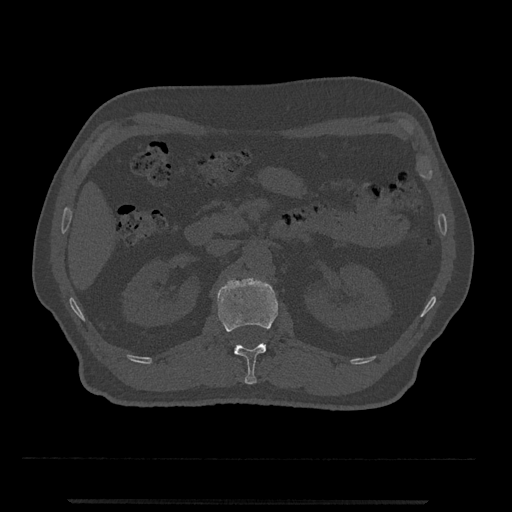
CT including the spine, one axial slice. Position 321 of 797 along the scan axis. 120 kVp. Bone window (W 1800 / L 400 HU). 0.5 mm slice thickness. 512 × 512 image matrix, field of view 419 × 419 mm. Male patient, age 63 years. From the clinical record (not read from this slice): primary cancer: prostate.
Structures marked on this image (semi-automatically segmented with operator editing):
- L1 vertebra: bounding box [x1, y1, x2, y2] px = [217, 277, 278, 385]